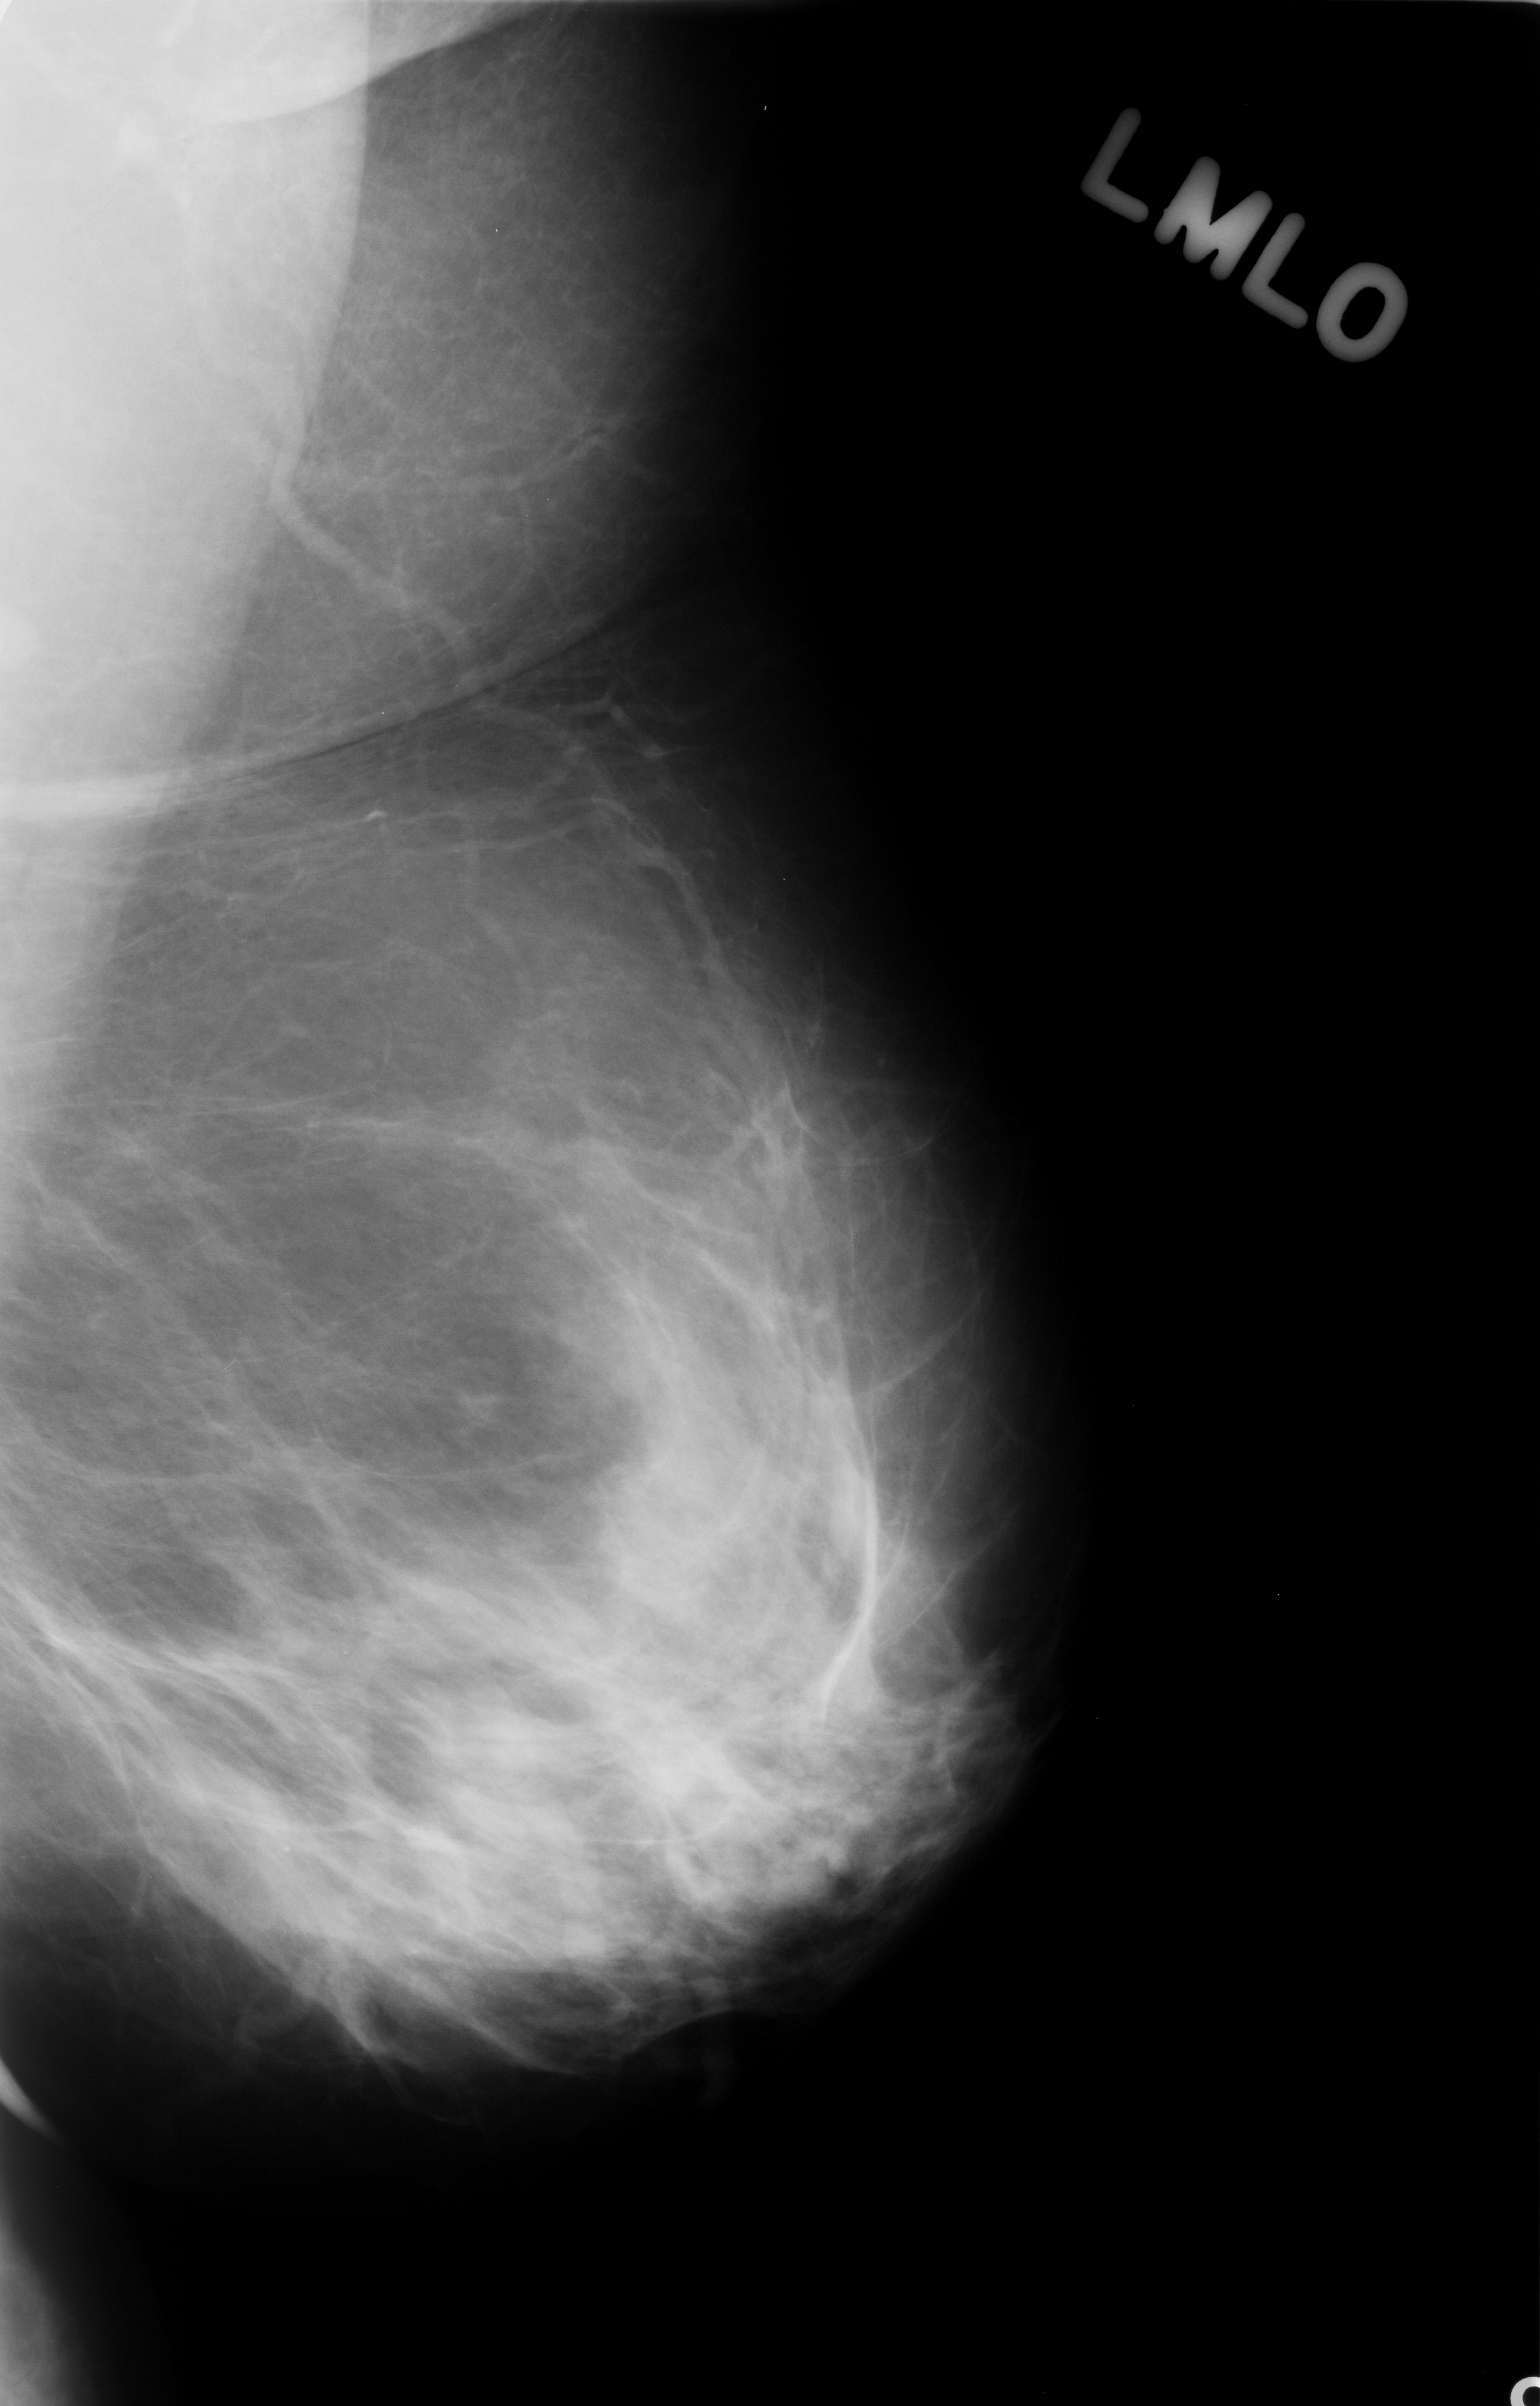
Mammogram (digitized film); left breast; MLO view; breast composition: scattered fibroglandular densities (BI-RADS density category 2 of 4).
- Abnormality record for this image: calcifications, morphology amorphous, distribution segmental; BI-RADS assessment category 4; pathology (as recorded): benign.